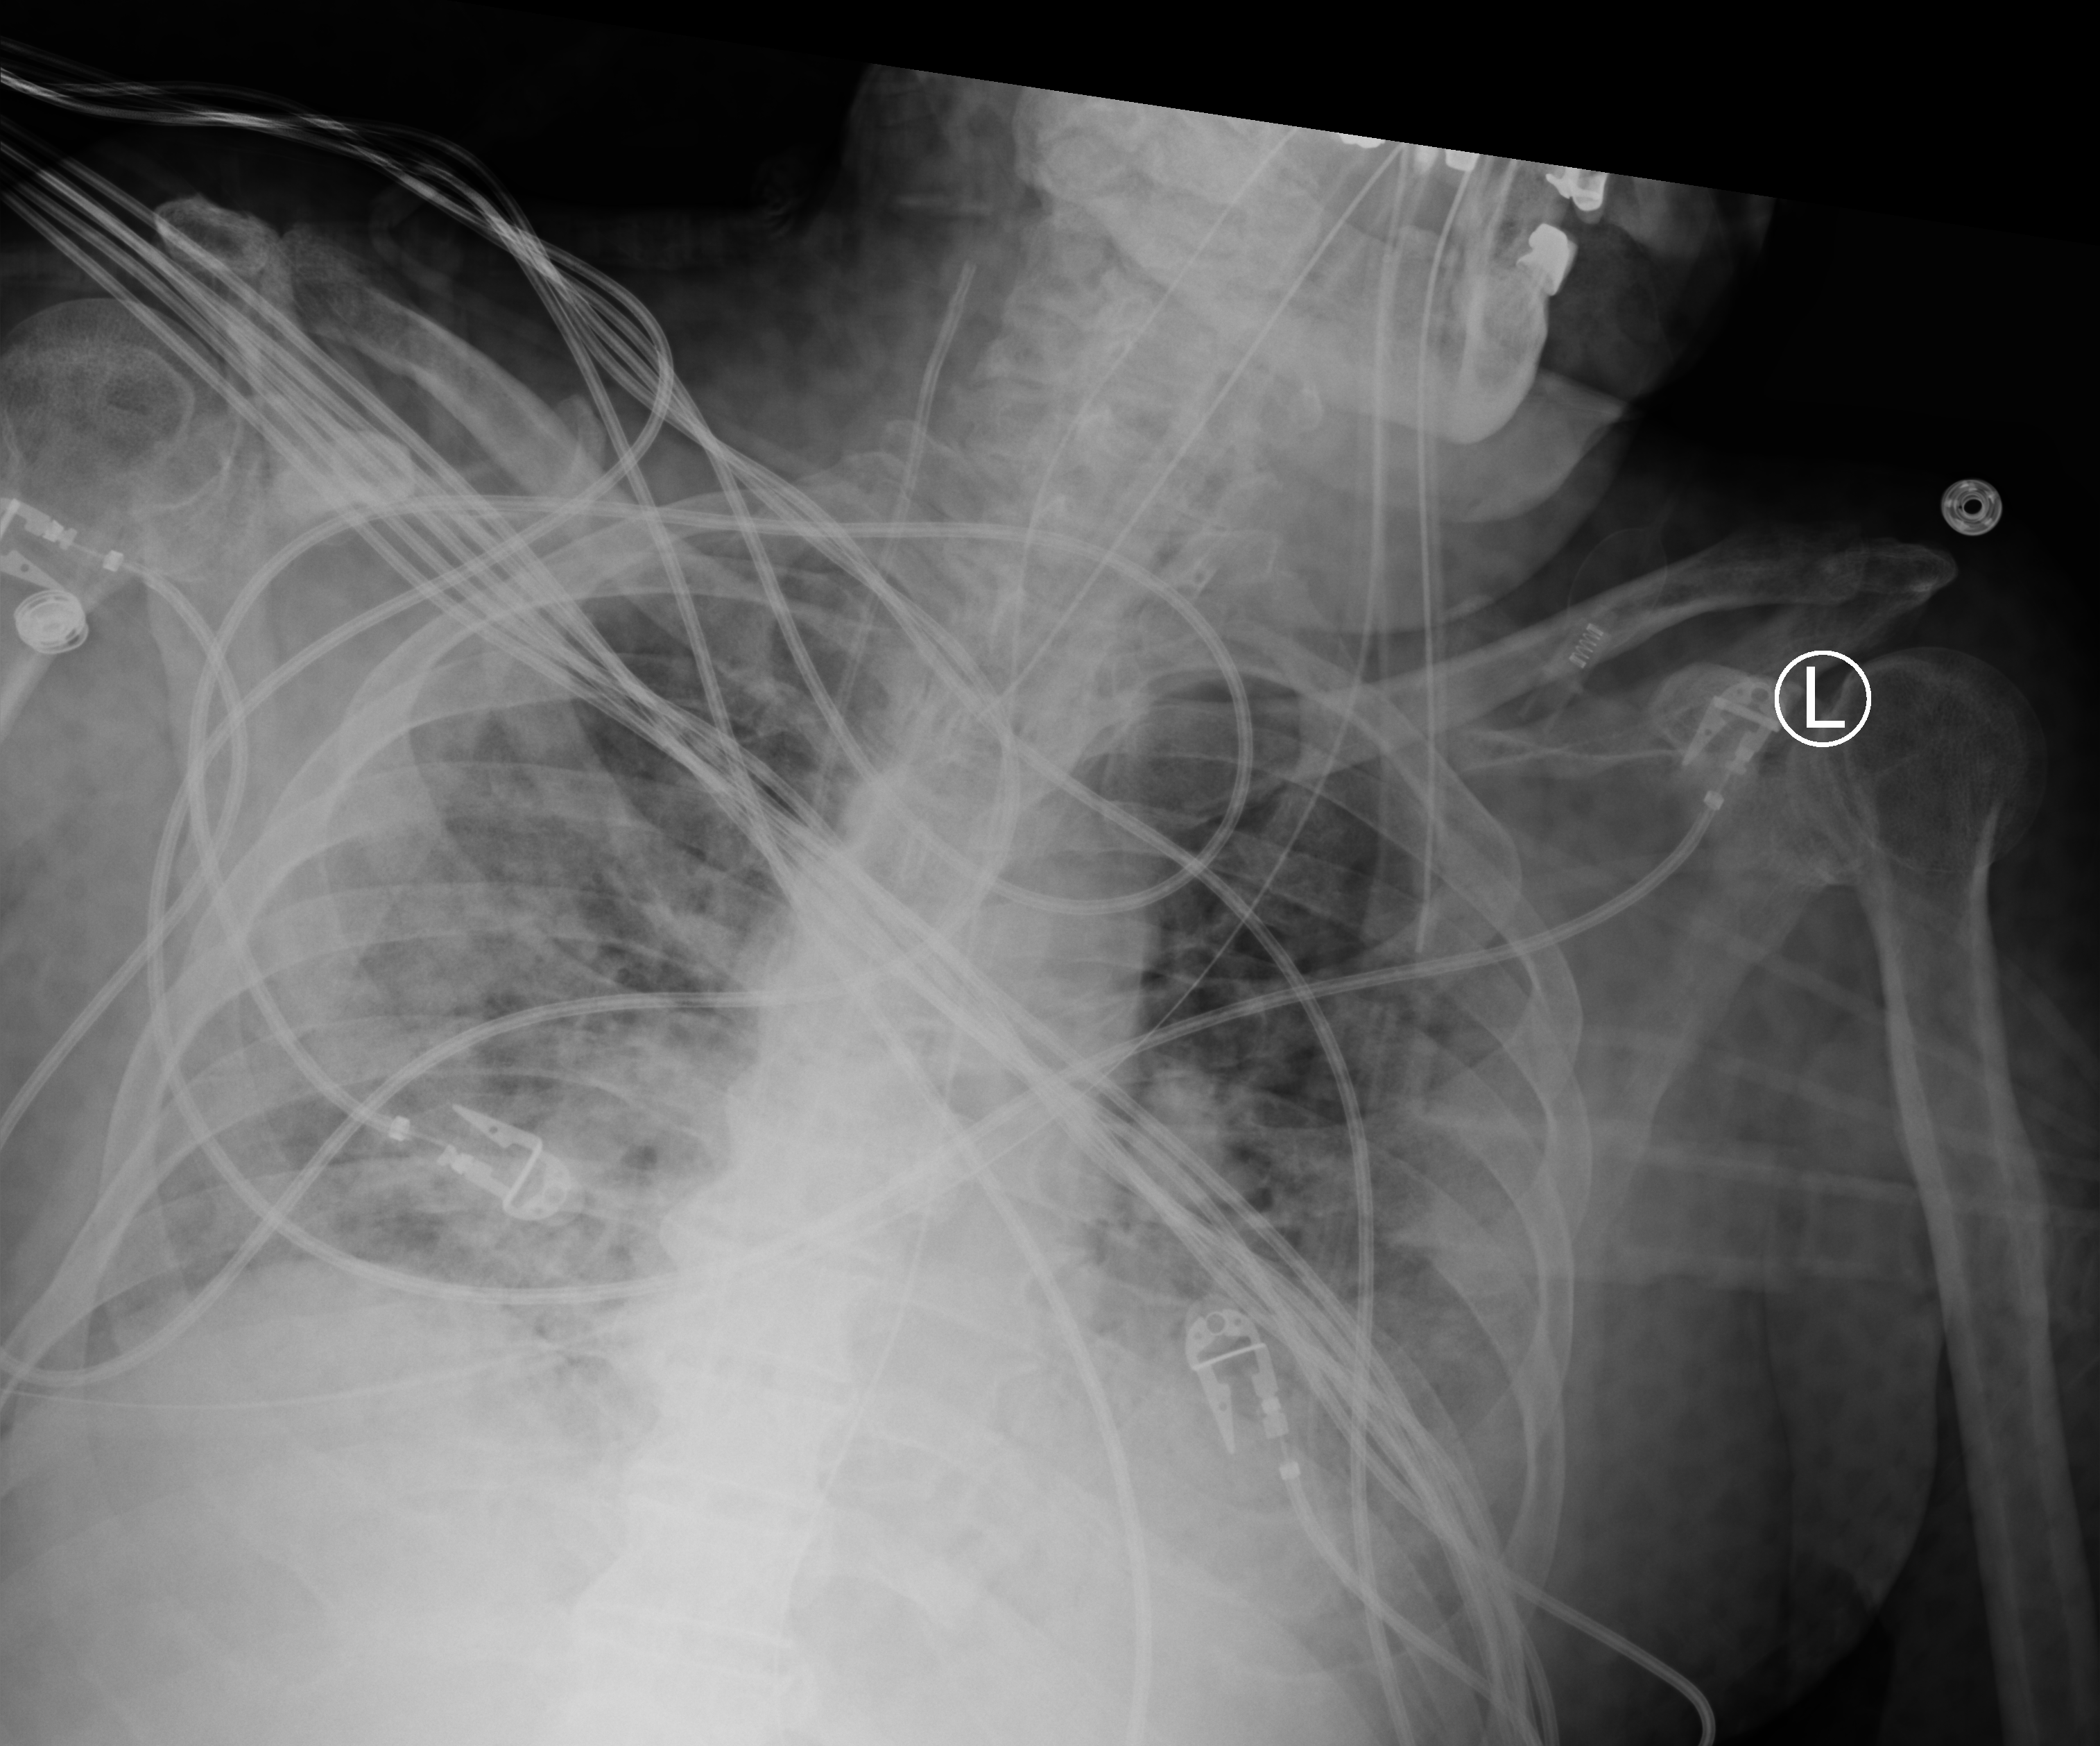
Chest X-ray (portable); anteroposterior (AP) projection. Male patient hospitalised with COVID-19, age 75–90 years.
Hospital-stay facts (about this admission, not read from this image; timing relative to this image not recorded):
- smoking status (admission record): former